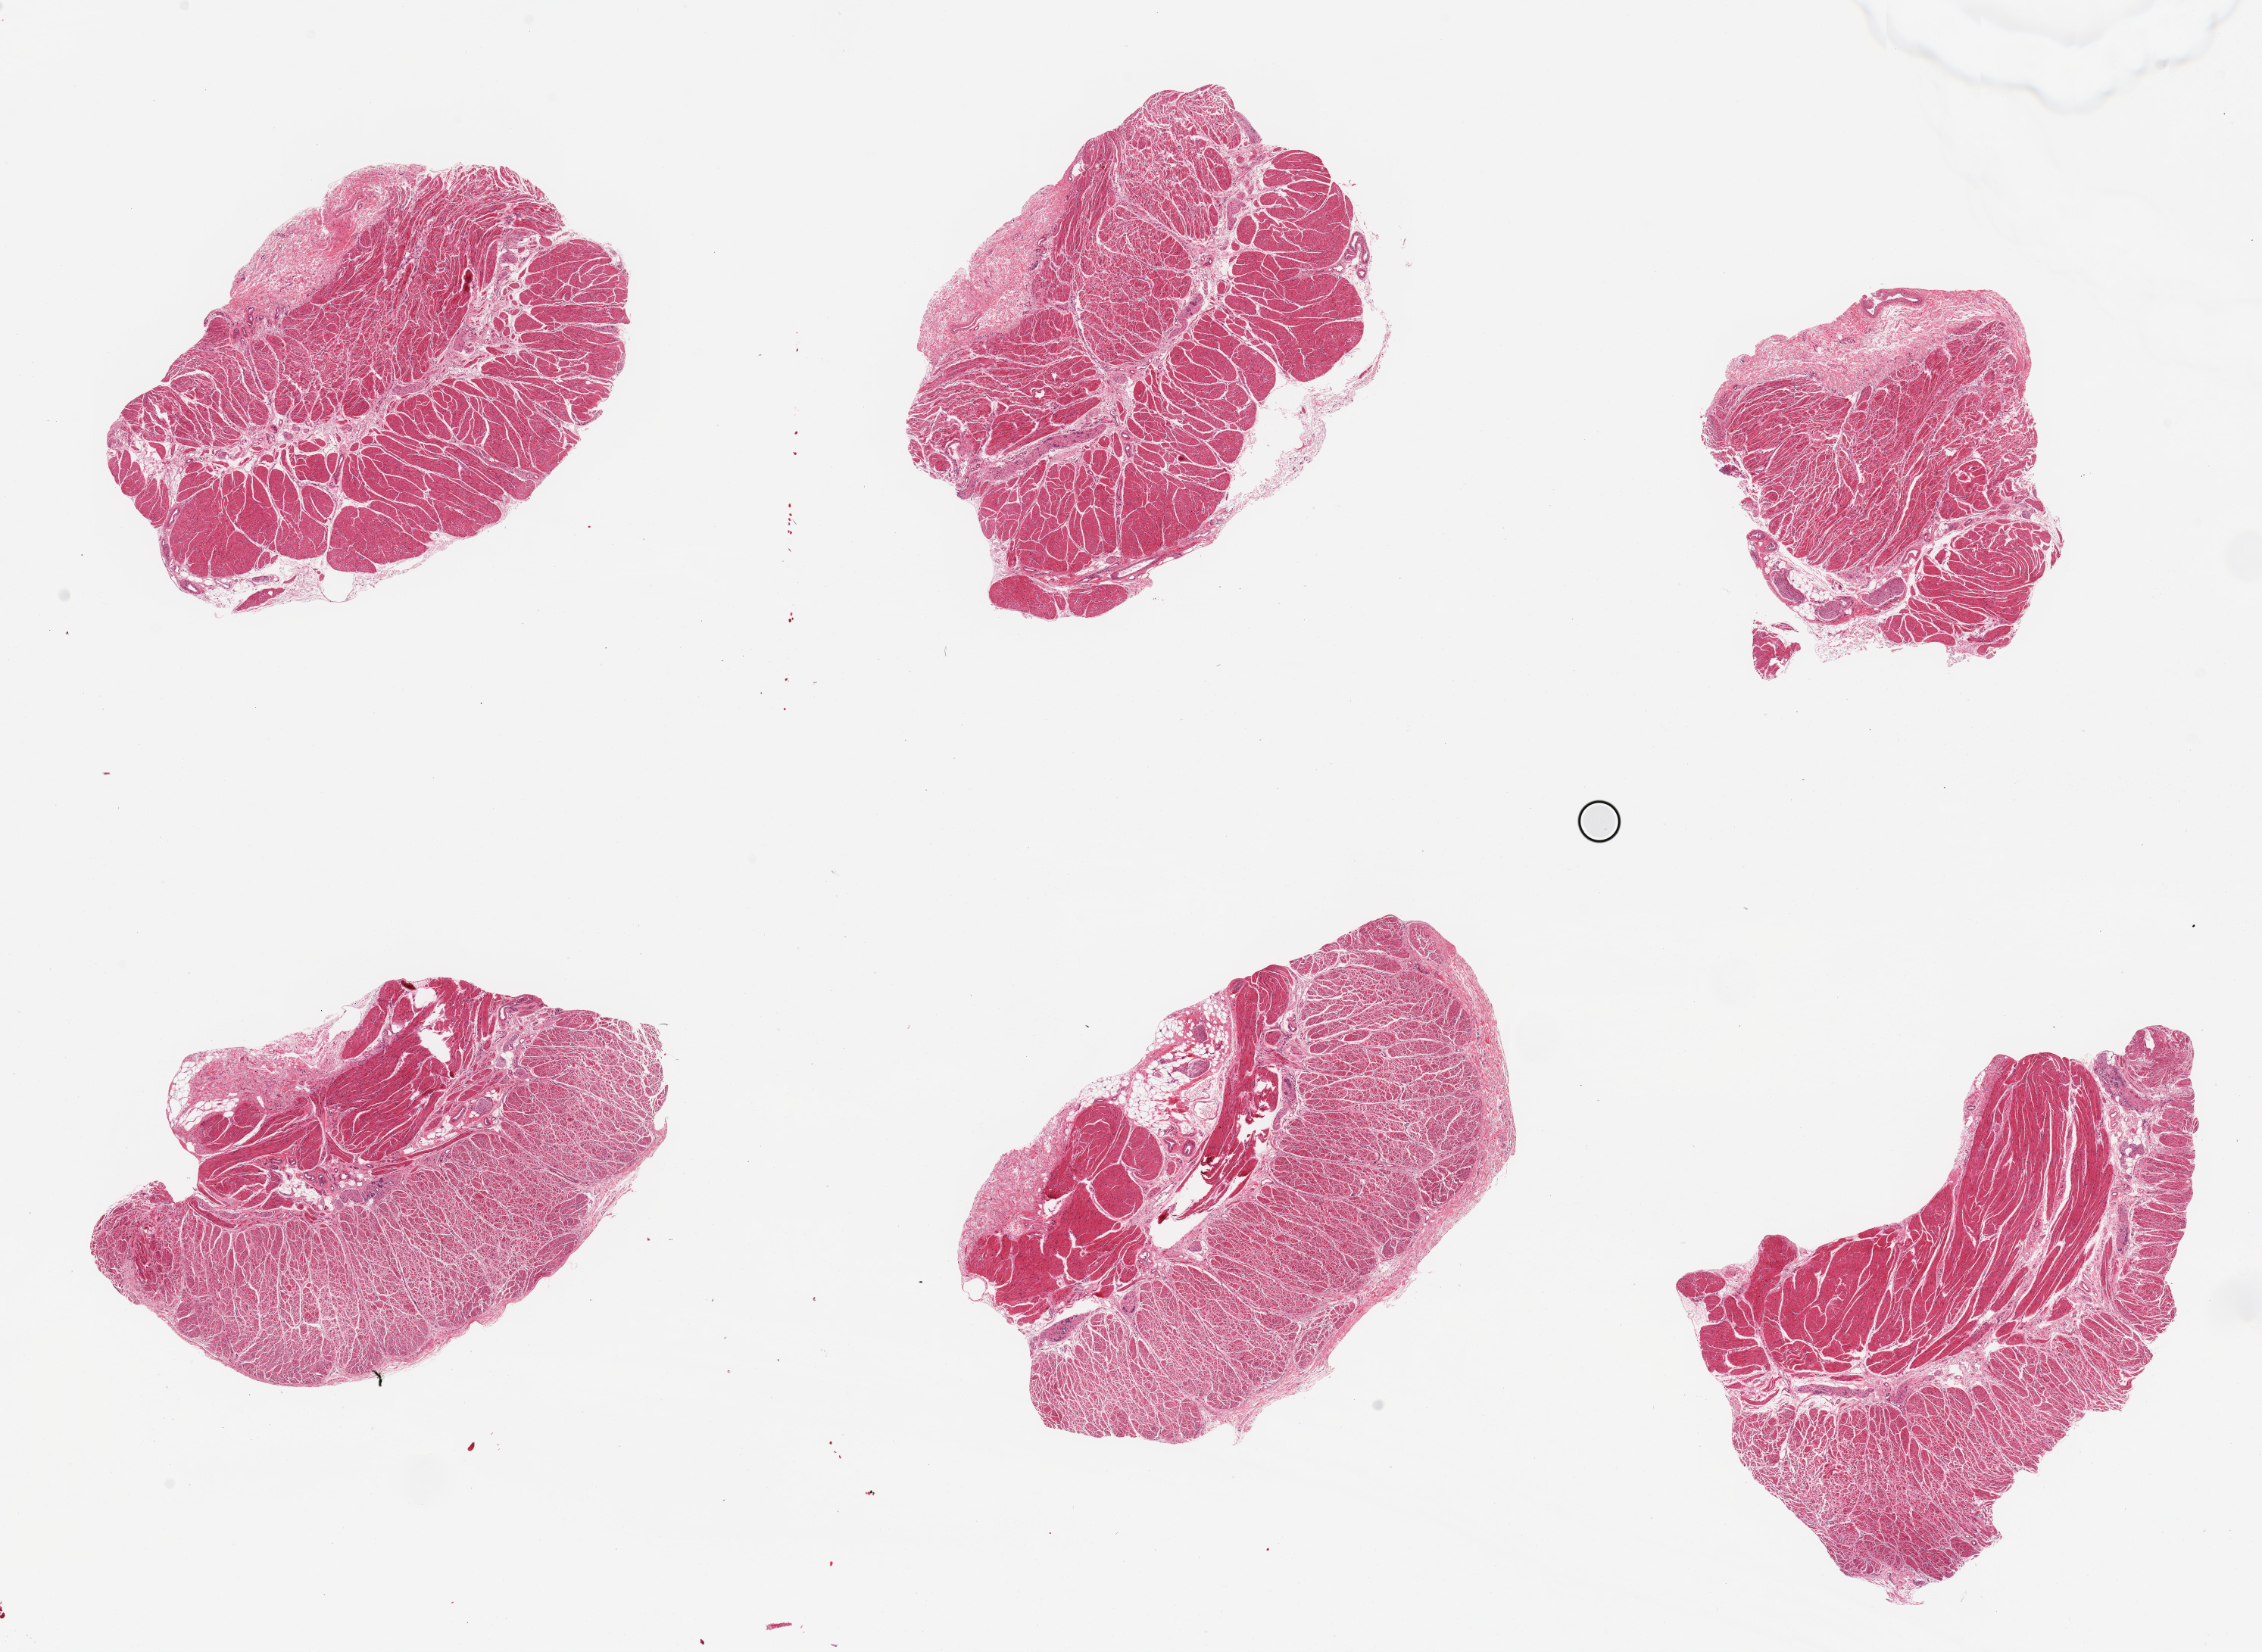
H&E whole-slide image, low-resolution overview of the scanned area, about 23.6 x 17.3 mm (from a 20x scan); PAXgene-fixed, paraffin-embedded tissue; target tissue: gastroesophageal junction; donor tissue sample. Male donor.
Pathologist's review note for this sample: 6 pieces; well dissected muscle.